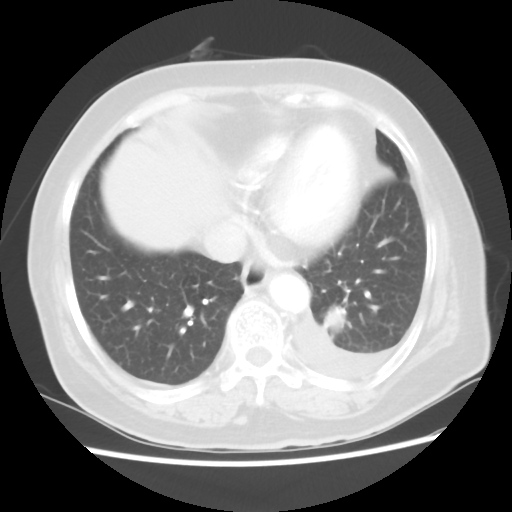
Chest CT, one axial slice; position 15 of 80 along the scan axis; reconstruction kernel STANDARD; lung window (W 1500 / L -600 HU); 5 mm slice thickness; 512 × 512 image matrix, field of view 343 × 343 mm. Patient: female, 68 years. Case-level facts recorded for this patient, not image findings: clinical TNM (as recorded): T1c N0 M1.
Annotated regions visible in this slice (rectangle marked by the reading radiologist):
- lung tumour (recorded histology: adenocarcinoma): box from (x=312, y=303) to (x=352, y=339) px